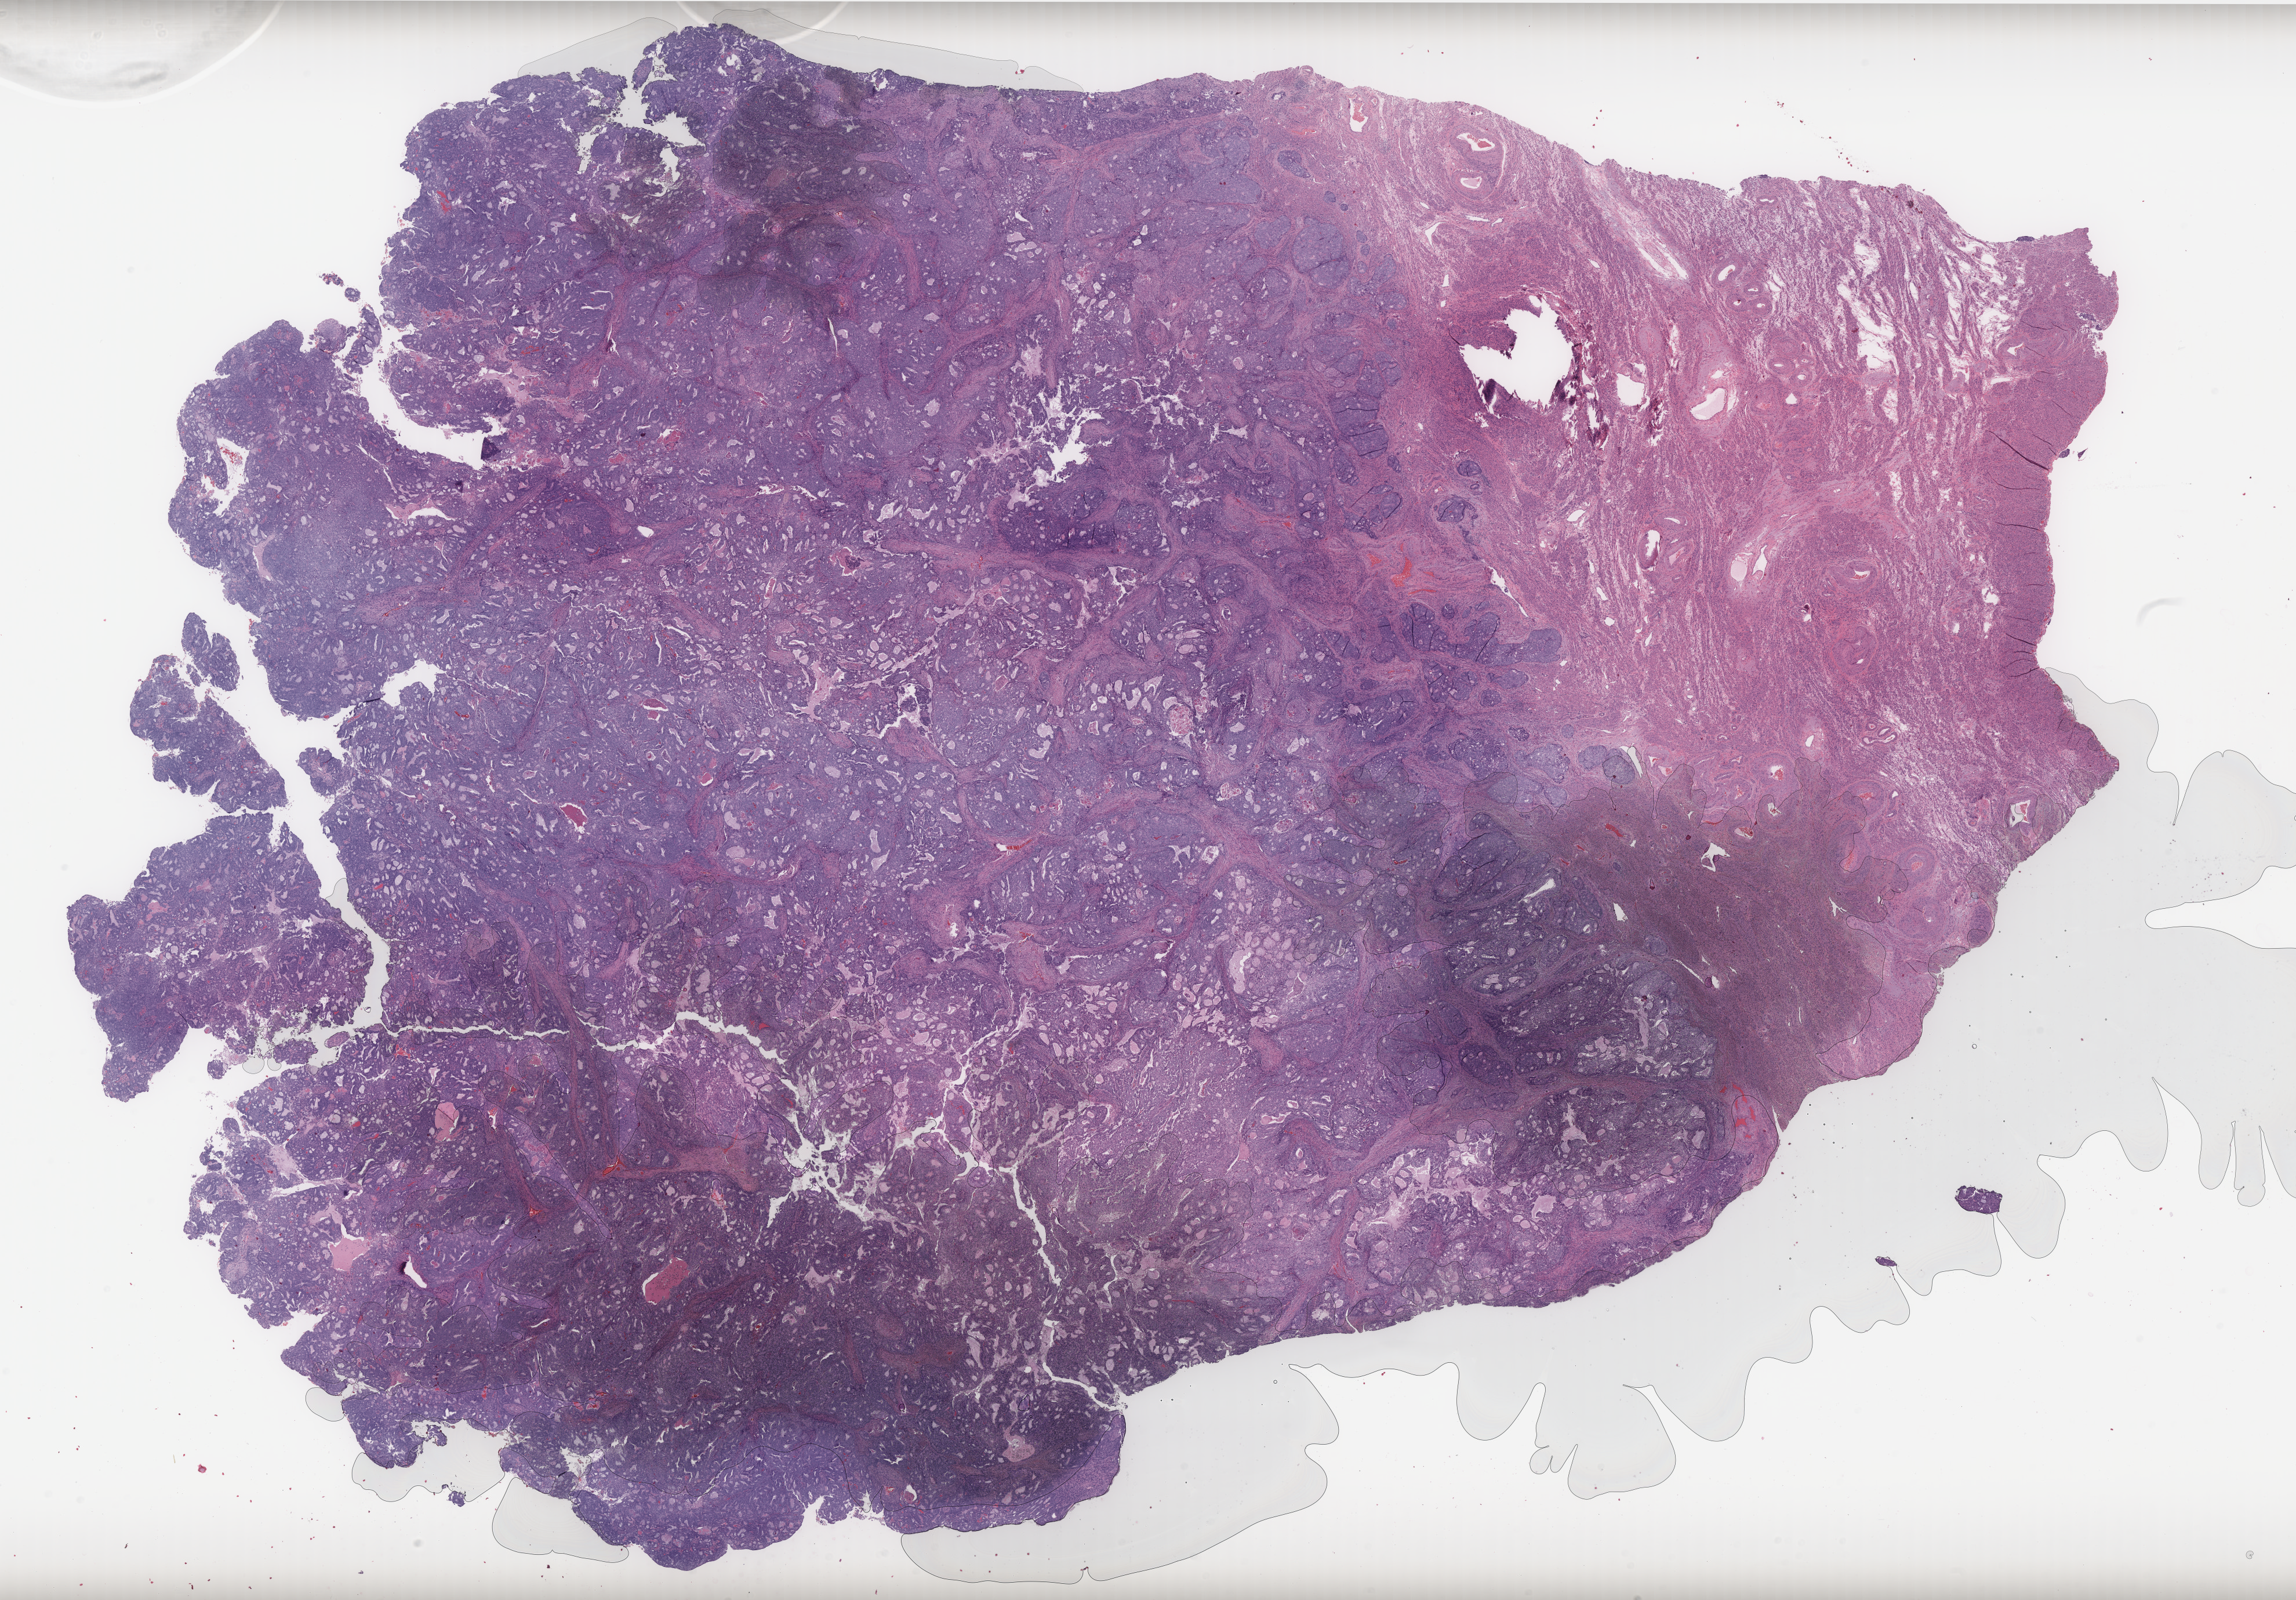
Whole-slide histology image, H&E, low-resolution overview of the scanned area, about 31.7 x 22.1 mm; formalin-fixed paraffin-embedded (FFPE) diagnostic section; sample: primary tumour, uterus. Patient: female, age at initial diagnosis 74 years. Histologic grade: G2 (moderately differentiated).
Lymph nodes positive (case pathology): 0 of 12 examined. Histologic diagnosis: Endometrioid adenocarcinoma, NOS (endometrium). FIGO stage: IB.